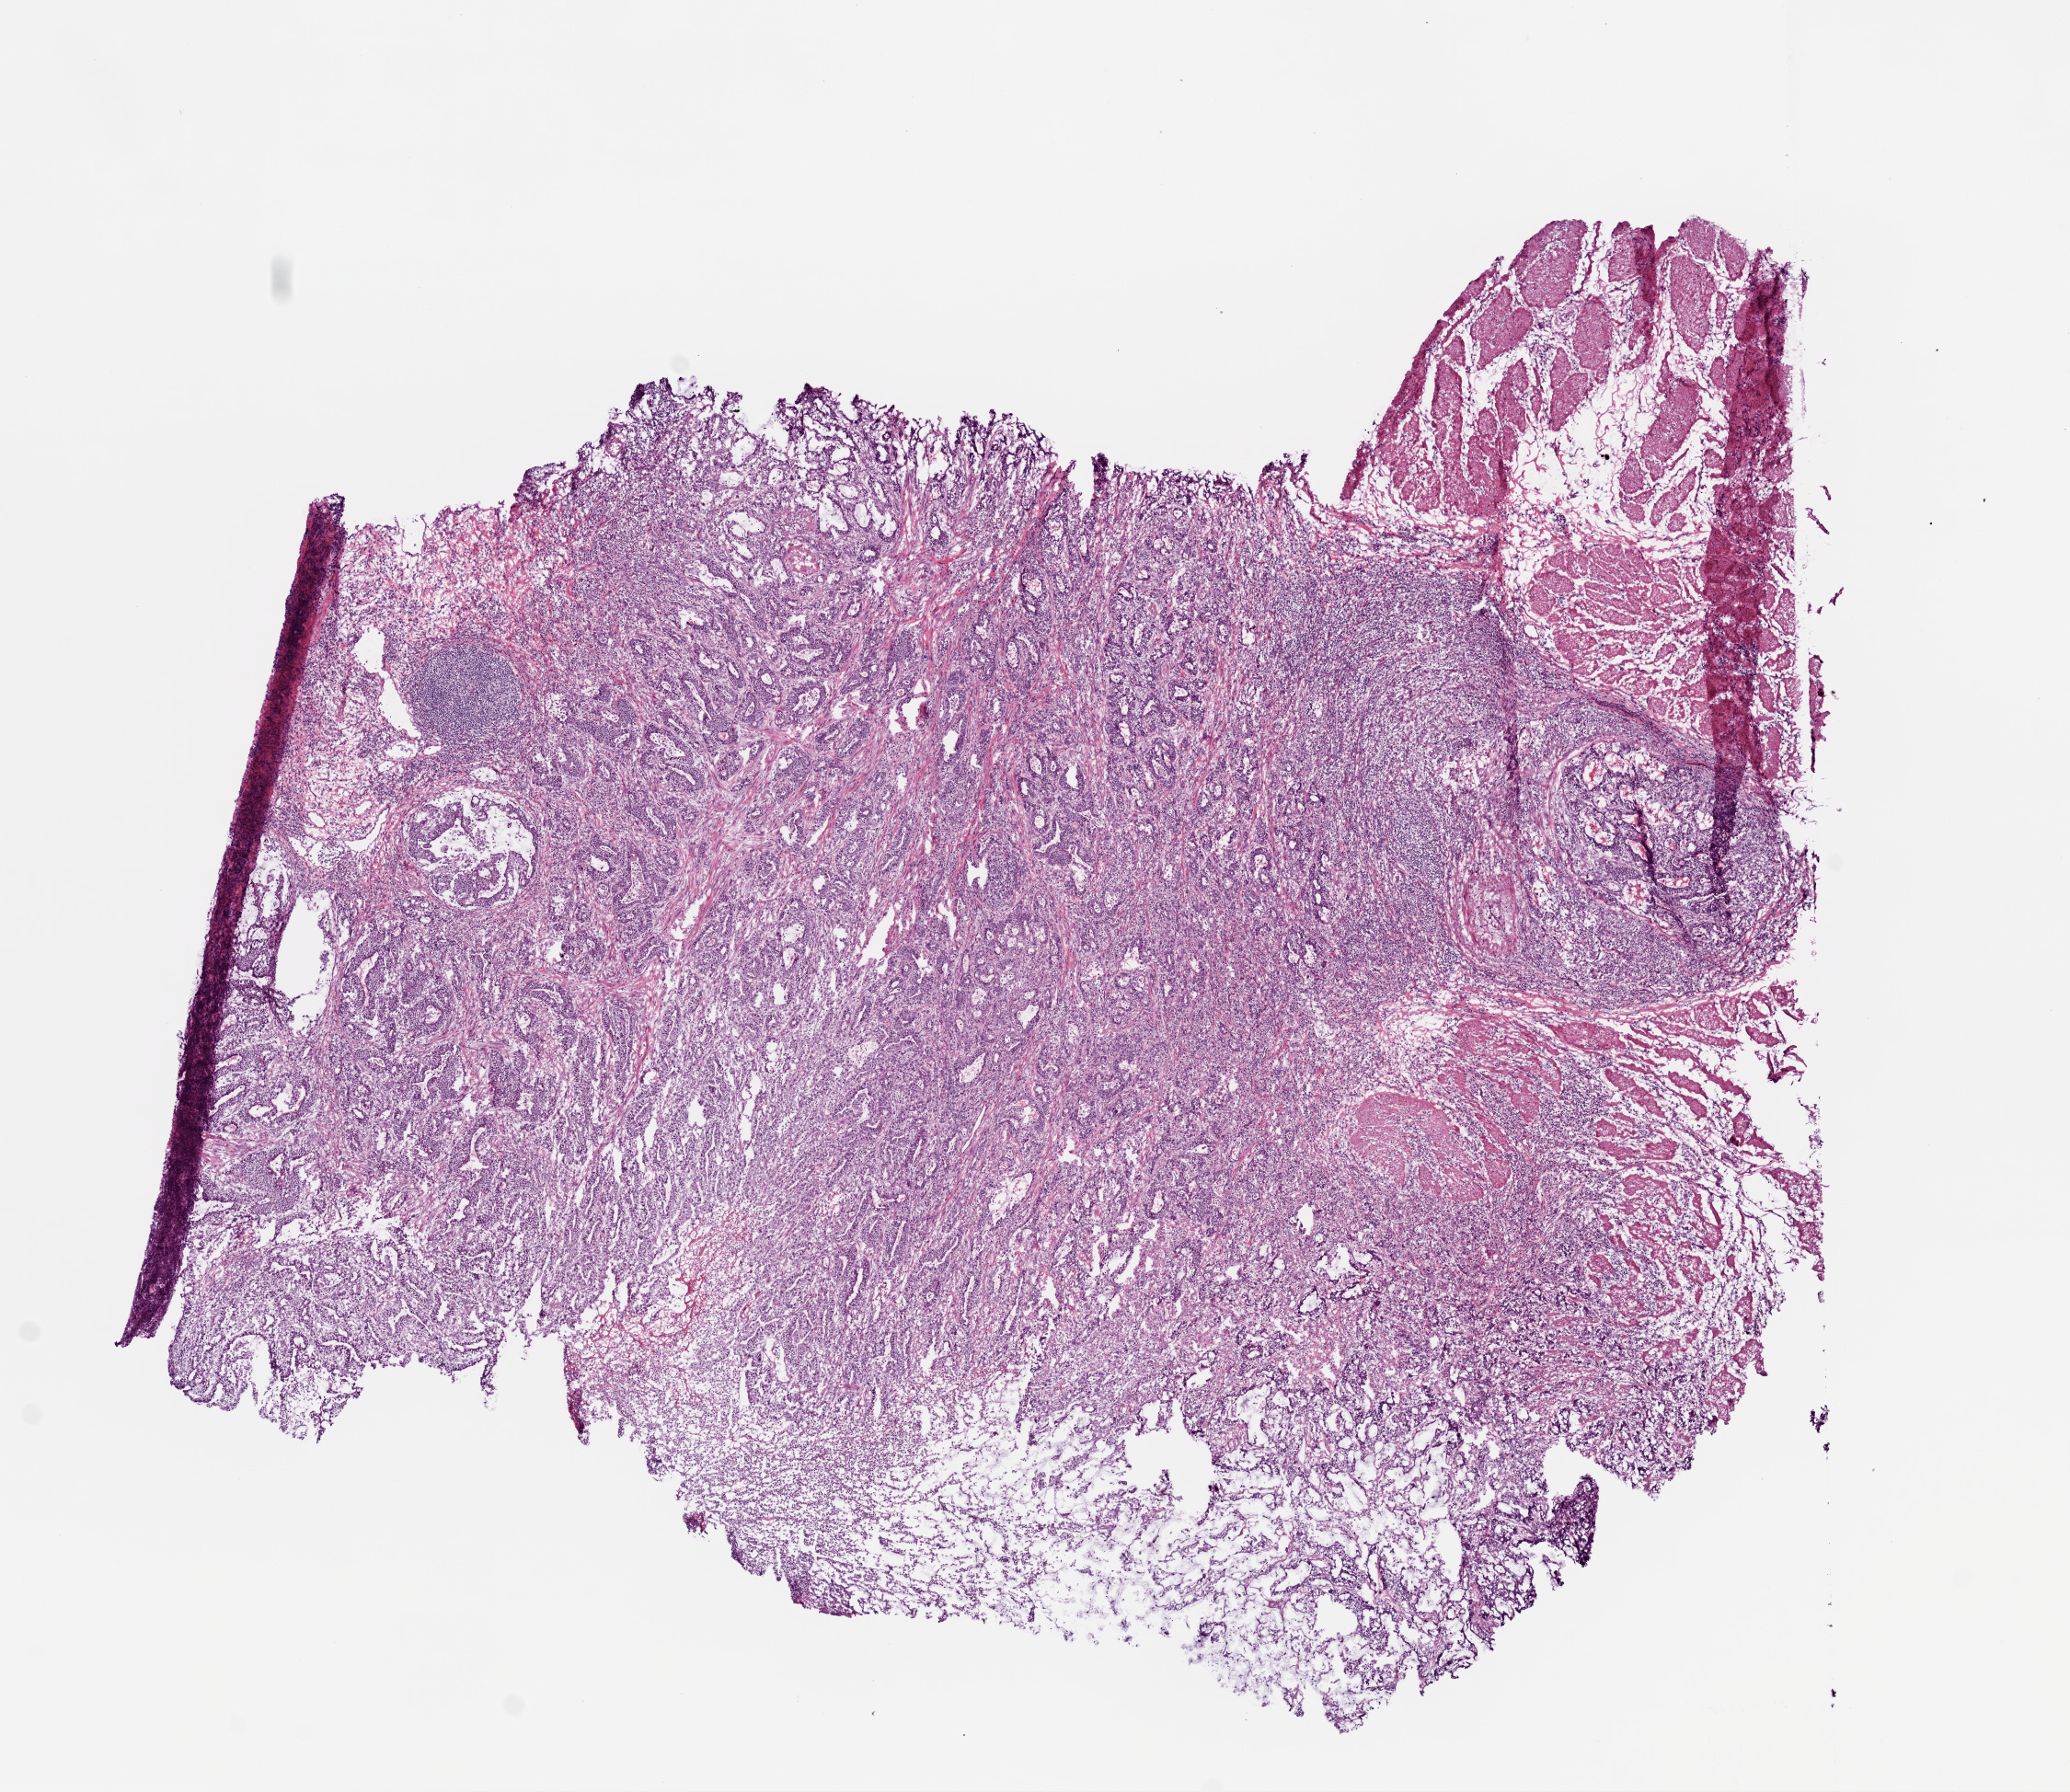
Whole-slide histology image, H&E-stained, shown as a low-resolution overview of the whole scanned area (about 9.0 x 7.8 mm, from a 20x scan), frozen section from the bottom of the tissue portion, primary tumour sample from the stomach. Female patient. Histologic grade: G3 (poorly differentiated). Composition of this section per pathologist review: tumour cells 70%, tumour nuclei 70%, normal cells 10%, stromal cells 10%, necrosis 5%.
Diagnosis: Adenocarcinoma, intestinal type (gastric antrum). AJCC pathologic stage: IB.